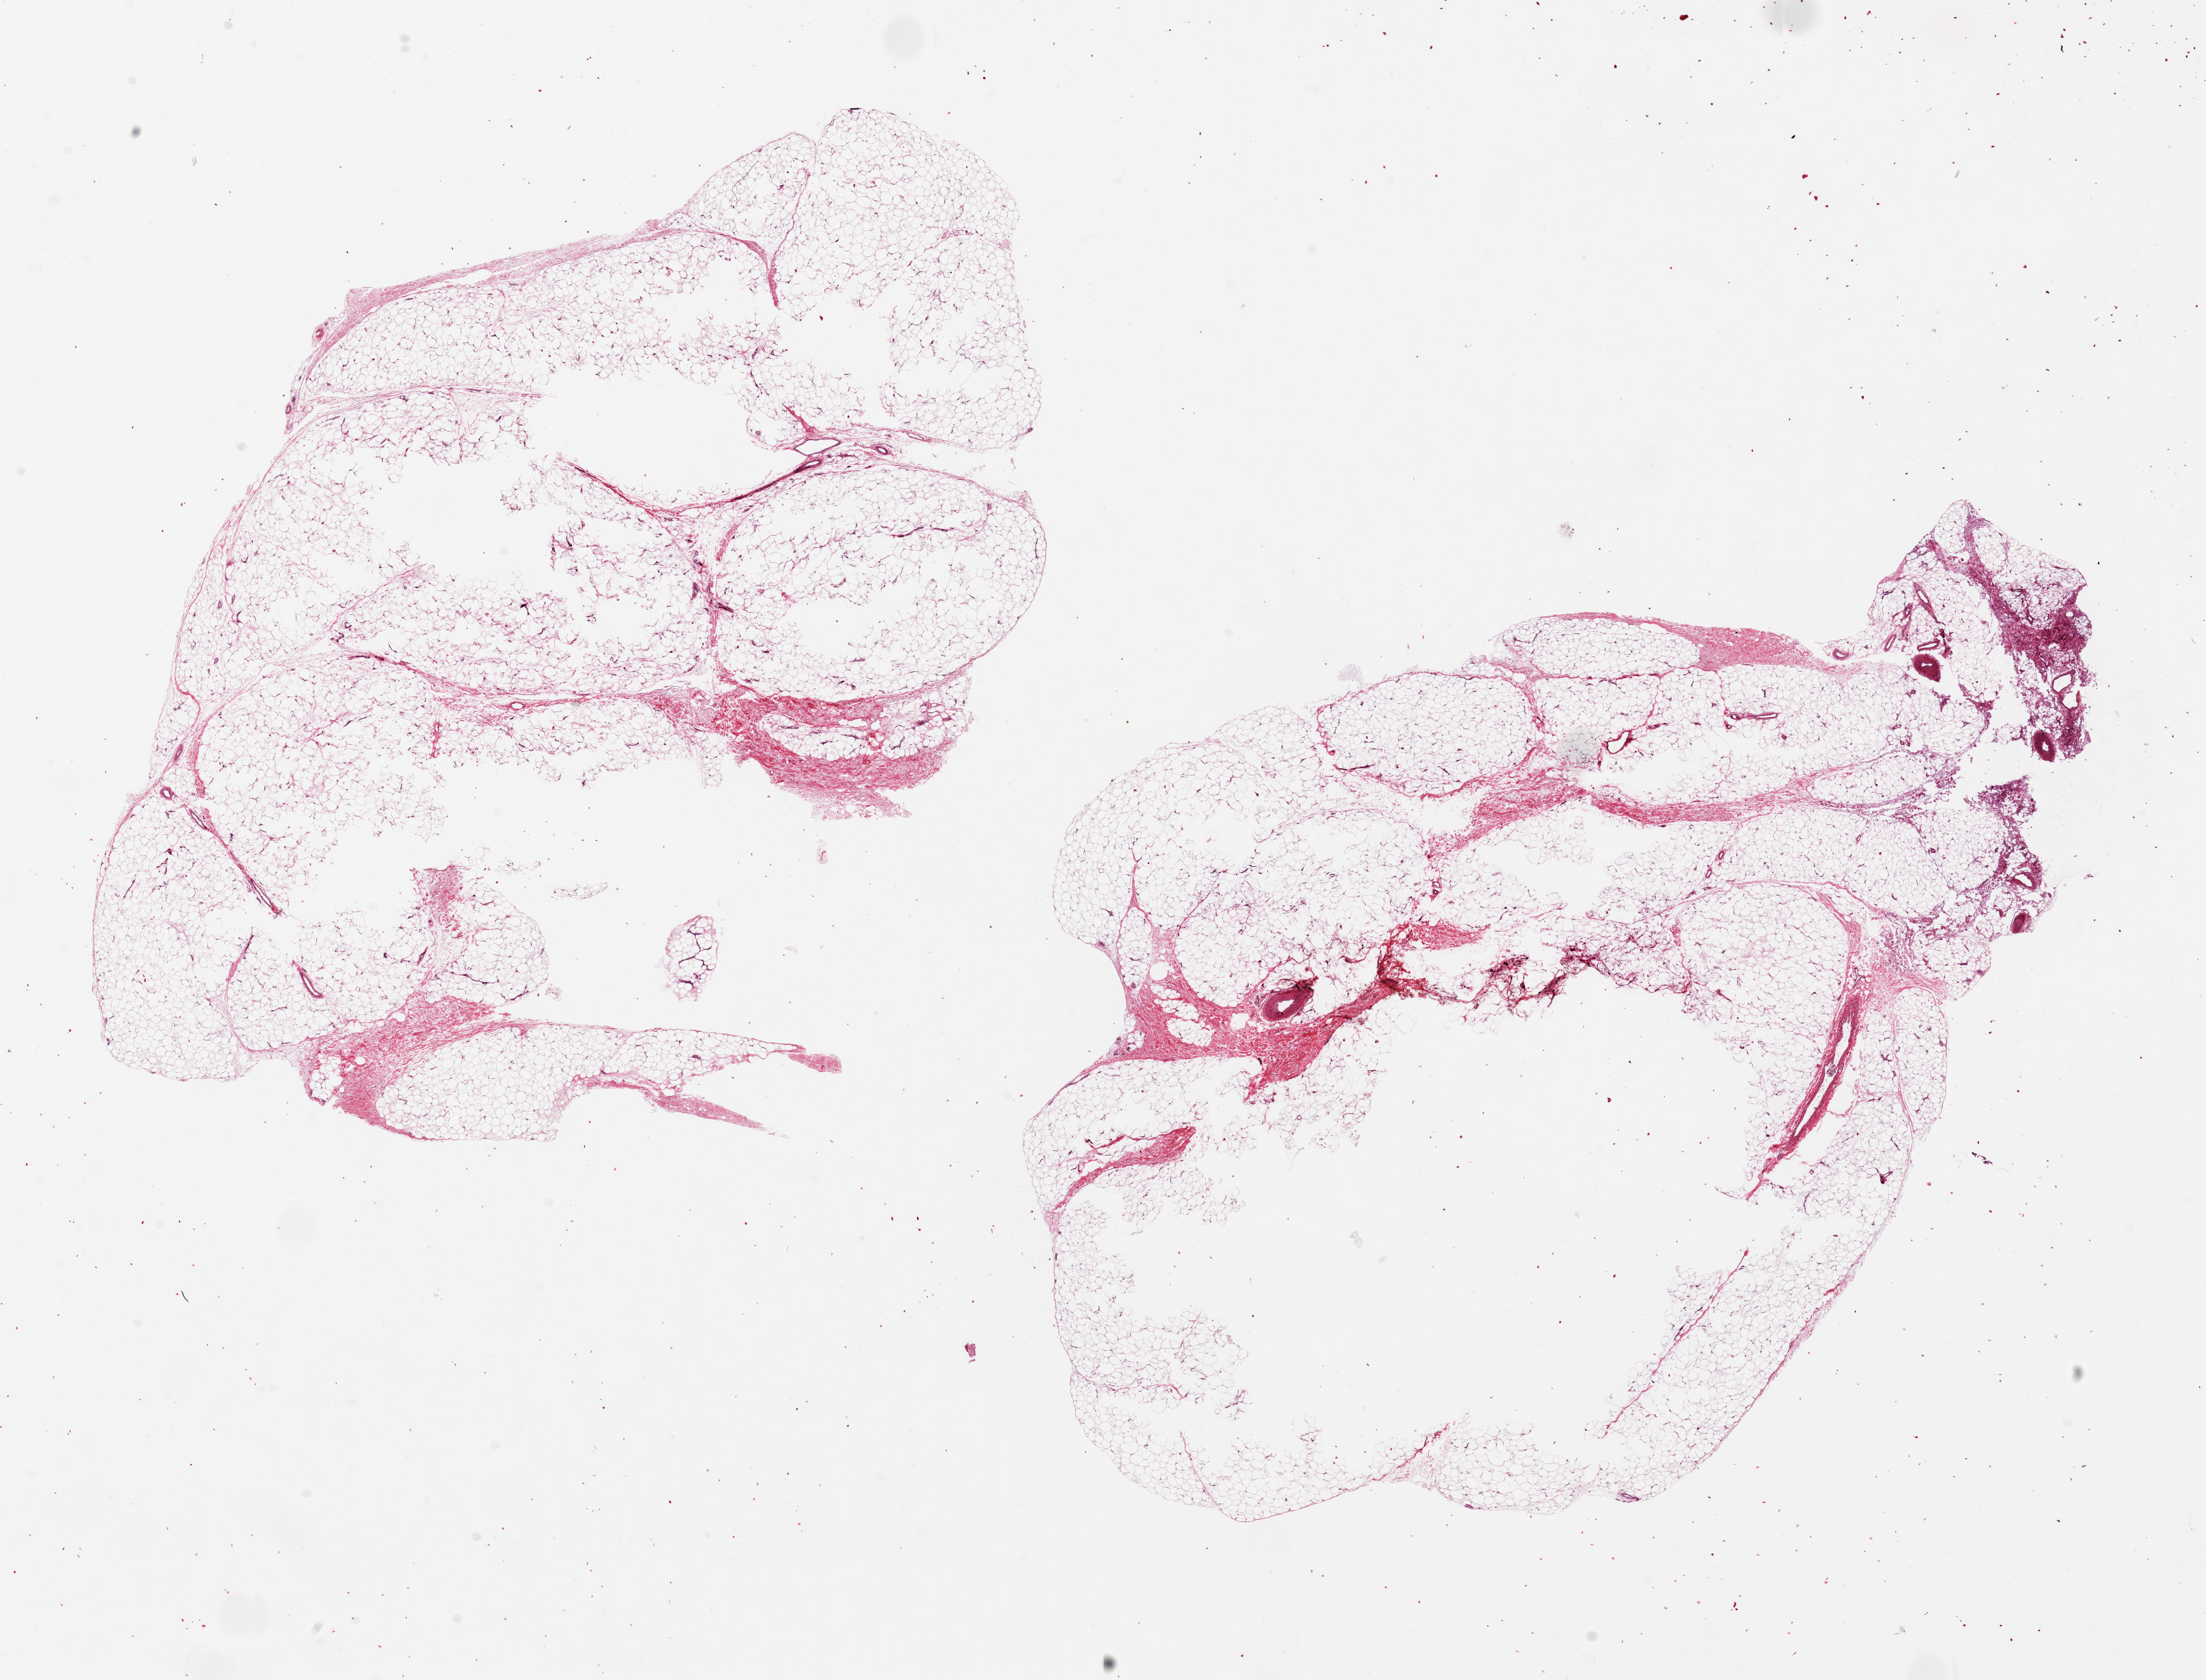
Digitized H&E-stained section, brightfield, whole scanned area (about 25.6 x 19.5 mm, acquisition: 20x scan) shown as a low-resolution overview, PAXgene-fixed, paraffin-embedded tissue, target tissue: adipose tissue, donor tissue sample.
* review note (as recorded): 2 pieces, 13x9 & 15x10mm; central hollow unfixed areas up to 6x4mm